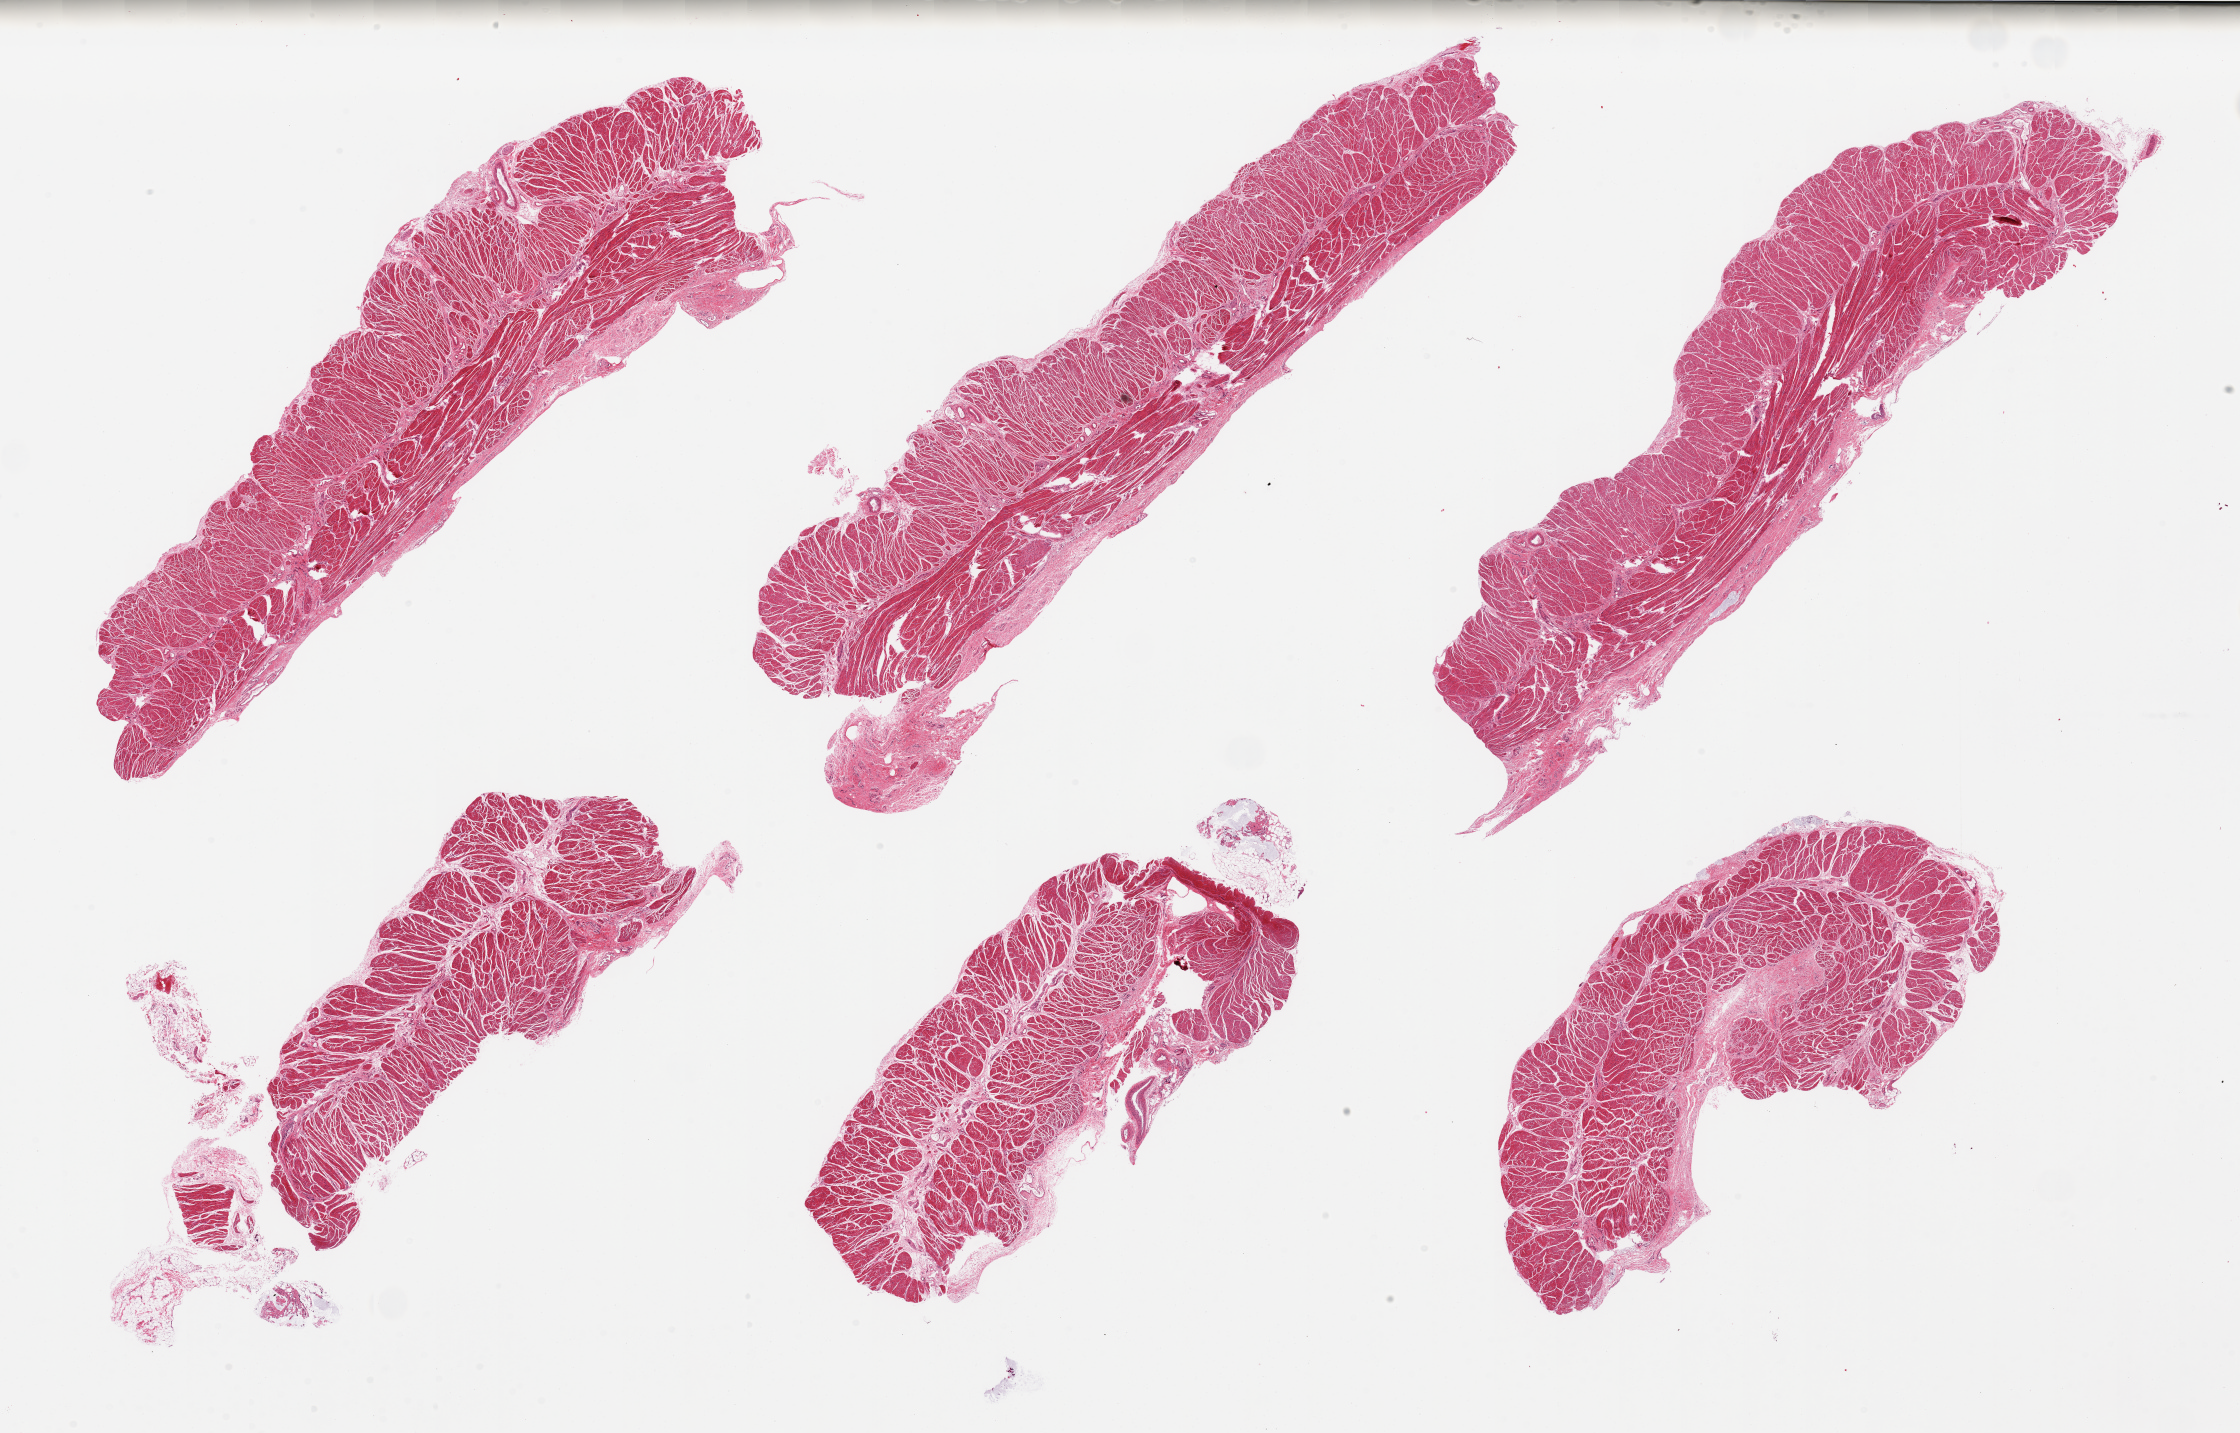
Whole-slide image, hematoxylin and eosin (H&E) stain — shown as a low-resolution overview of the whole scanned area (about 35.4 x 22.7 mm, acquisition: 20x scan). PAXgene-fixed paraffin-embedded (PFPE) section. Target tissue: esophageal muscle. Donor tissue sample. Female donor.
Review note (as recorded): 6 pieces, all muscularis, good specimens.